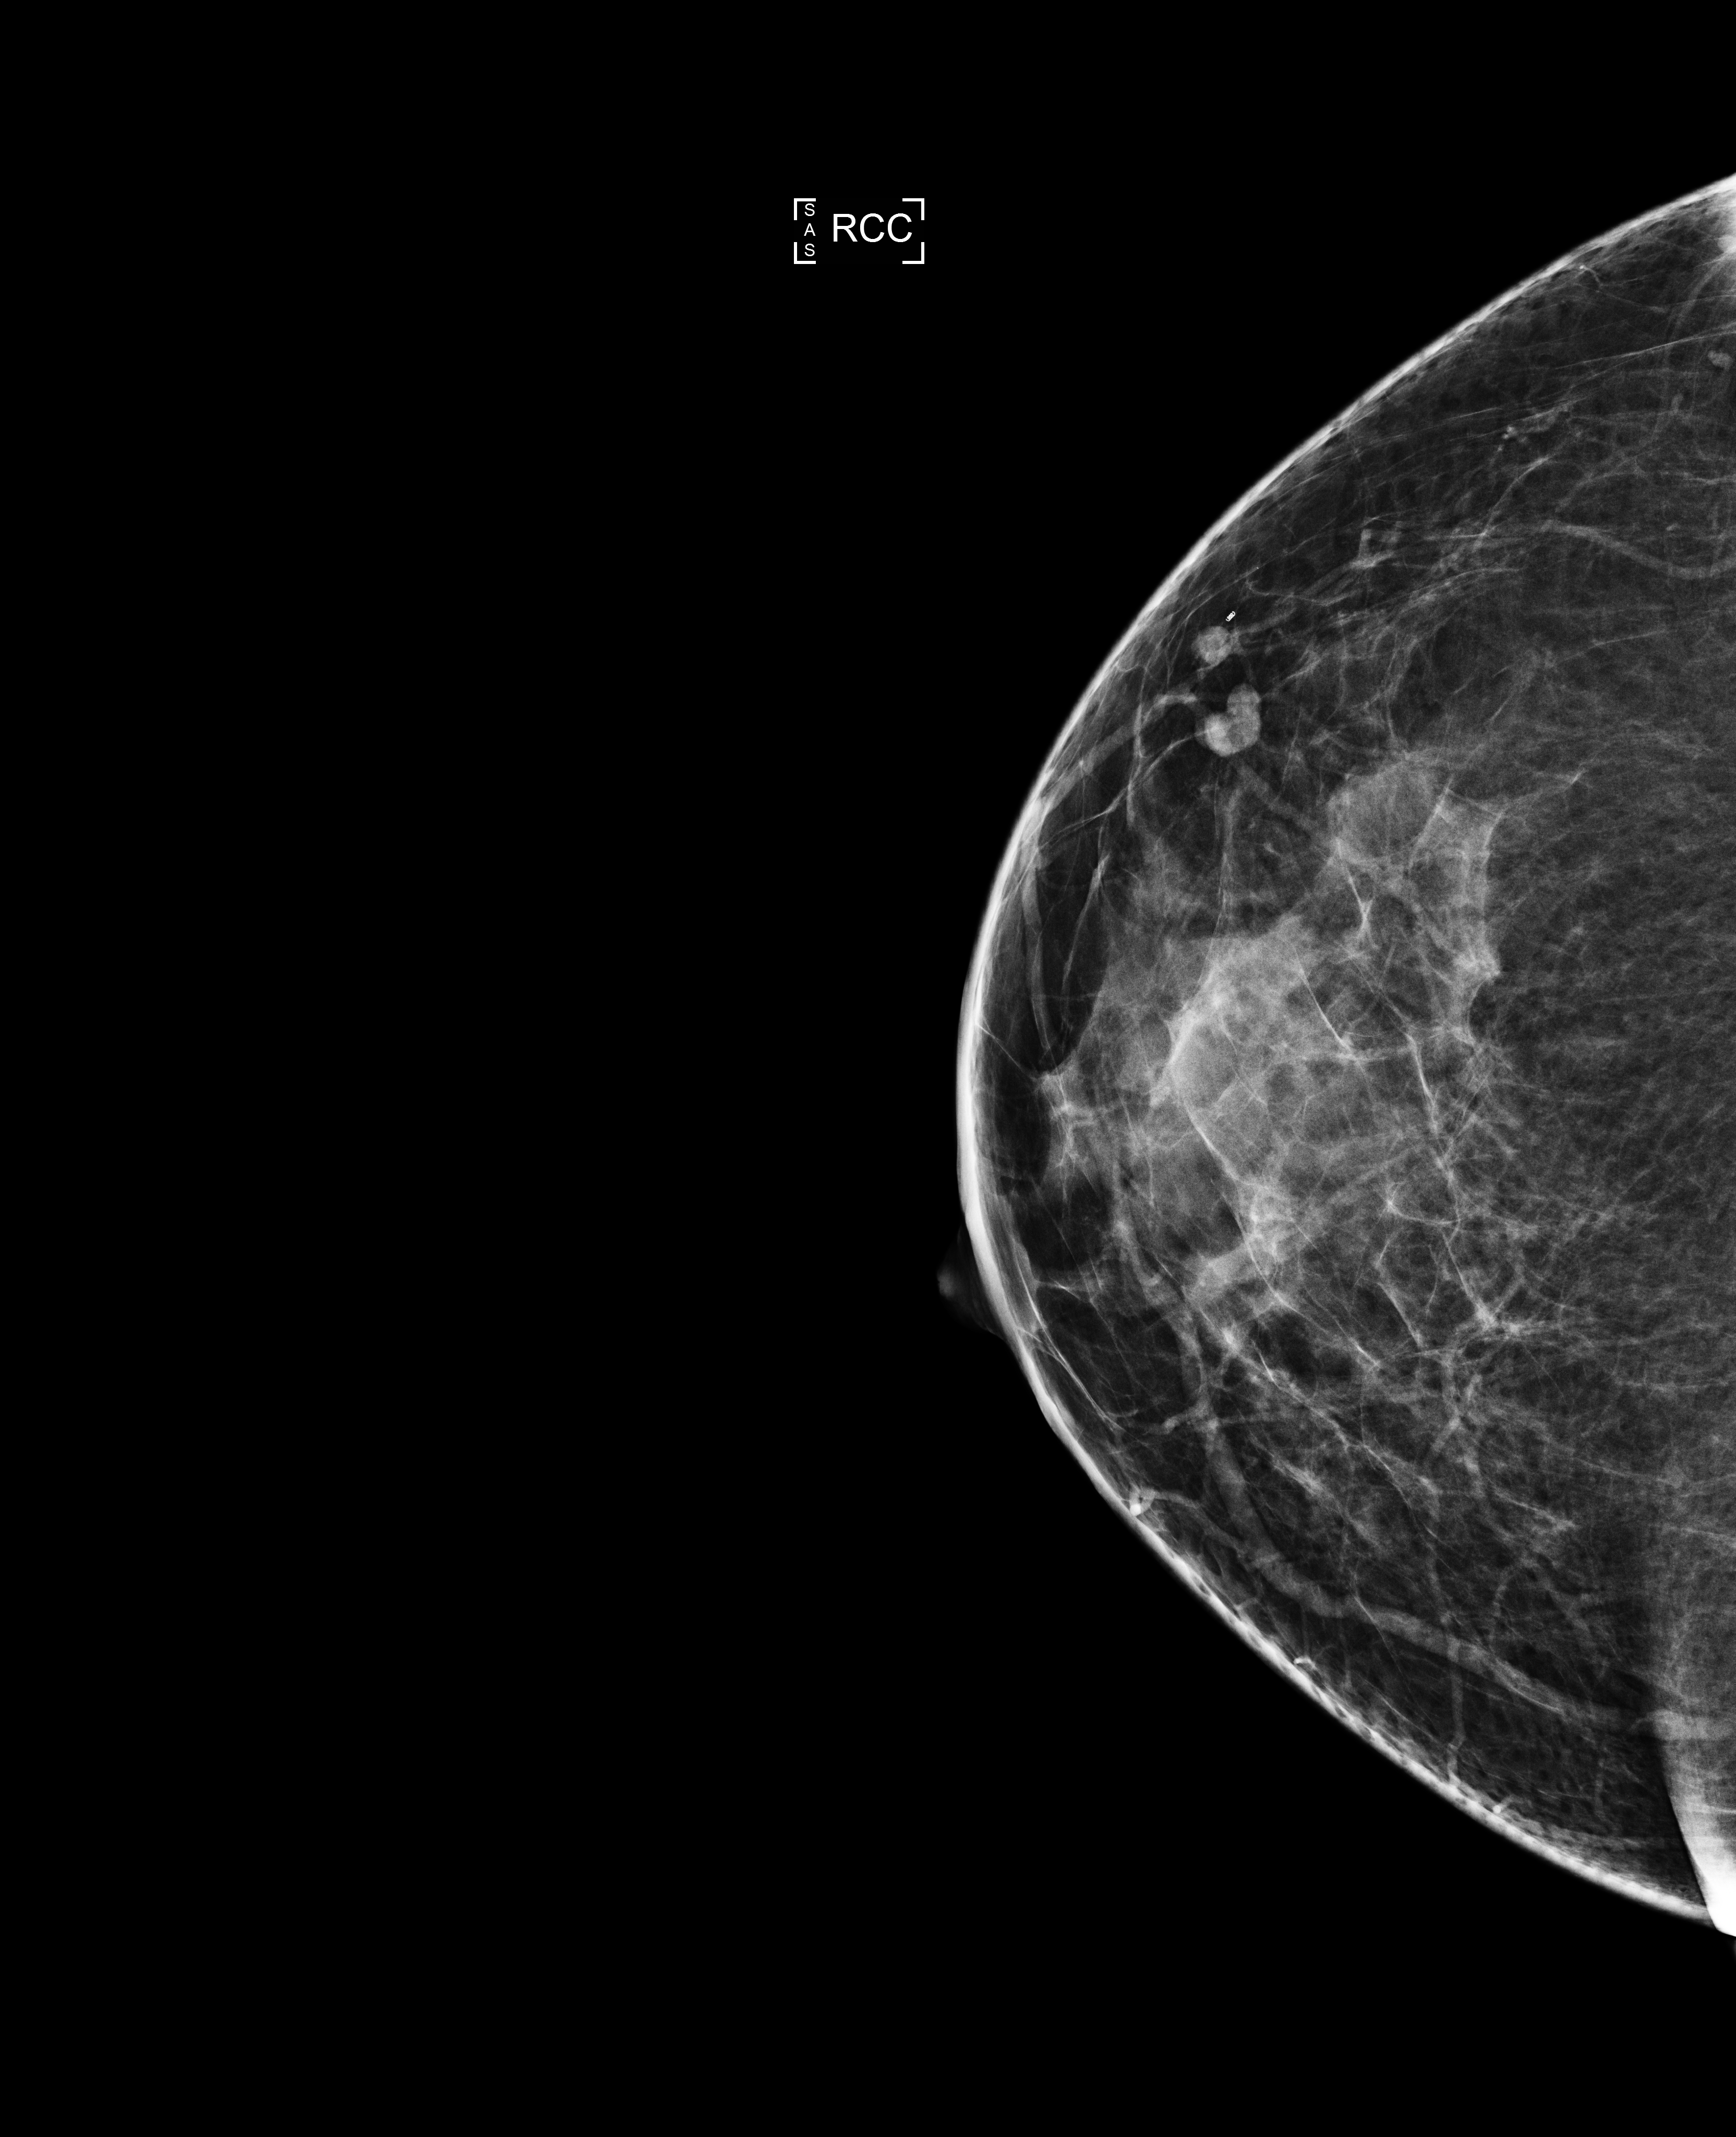
Digital mammogram (FFDM), right breast, cranio-caudal projection, annual screening mammography examination, compressed breast thickness 54 mm, system: Selenia Dimensions. Female patient, age 46 years.
BI-RADS breast density category at the screening exam (both breasts, scale 1–4): 3. Final BI-RADS assessment for this screening round (tomosynthesis exam, both breasts): category 1. Recall: no recall after this screen.